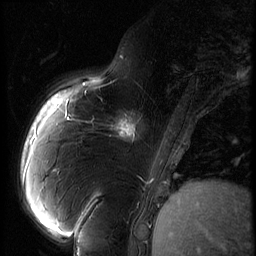
Breast MRI (dynamic contrast-enhanced), one sagittal slice. Position 18 of 60 along the scan axis. 3 images stored at this slice position (order not interpretable as contrast timing). 1.5 T. TE 4.2 ms, TR 9 ms. 2.5 mm slice thickness. 256 × 256 image matrix, field of view 180 × 180 mm. Female patient, age 57 years. Case-level facts recorded for this patient, not image findings: setting: breast cancer imaged before/during neoadjuvant chemotherapy; receptor status: triple-negative.
Outlined on this slice (semi-automatic segmentation, software-assisted and operator-edited):
- analysis volume of interest (the breast-tissue region the enhancement analysis was run in; not a lesion): bounding box <106,101,157,152> (left, top, right, bottom; pixels)
- tumour enhancement mask (voxels above the 140 % enhancement threshold inside the analysis volume of interest): <112,121,136,142>